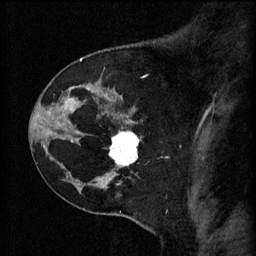
Breast MRI (dynamic contrast-enhanced), one sagittal slice. Position 44 of 60 along the scan axis. 3 images stored at this slice position (order not interpretable as contrast timing). 1.5 T. TE 4.2 ms, TR 11 ms. 256 × 256 image matrix, field of view 180 × 180 mm. Female patient, age 45 years.
Structures marked on this image (semi-automatic segmentation, software-assisted and operator-edited):
- analysis volume of interest (the breast-tissue region the enhancement analysis was run in; not a lesion): bounding box <110,130,143,171> (left, top, right, bottom; pixels)
- tumour enhancement mask (voxels above the 70 % enhancement threshold inside the analysis volume of interest): <110,132,139,167>